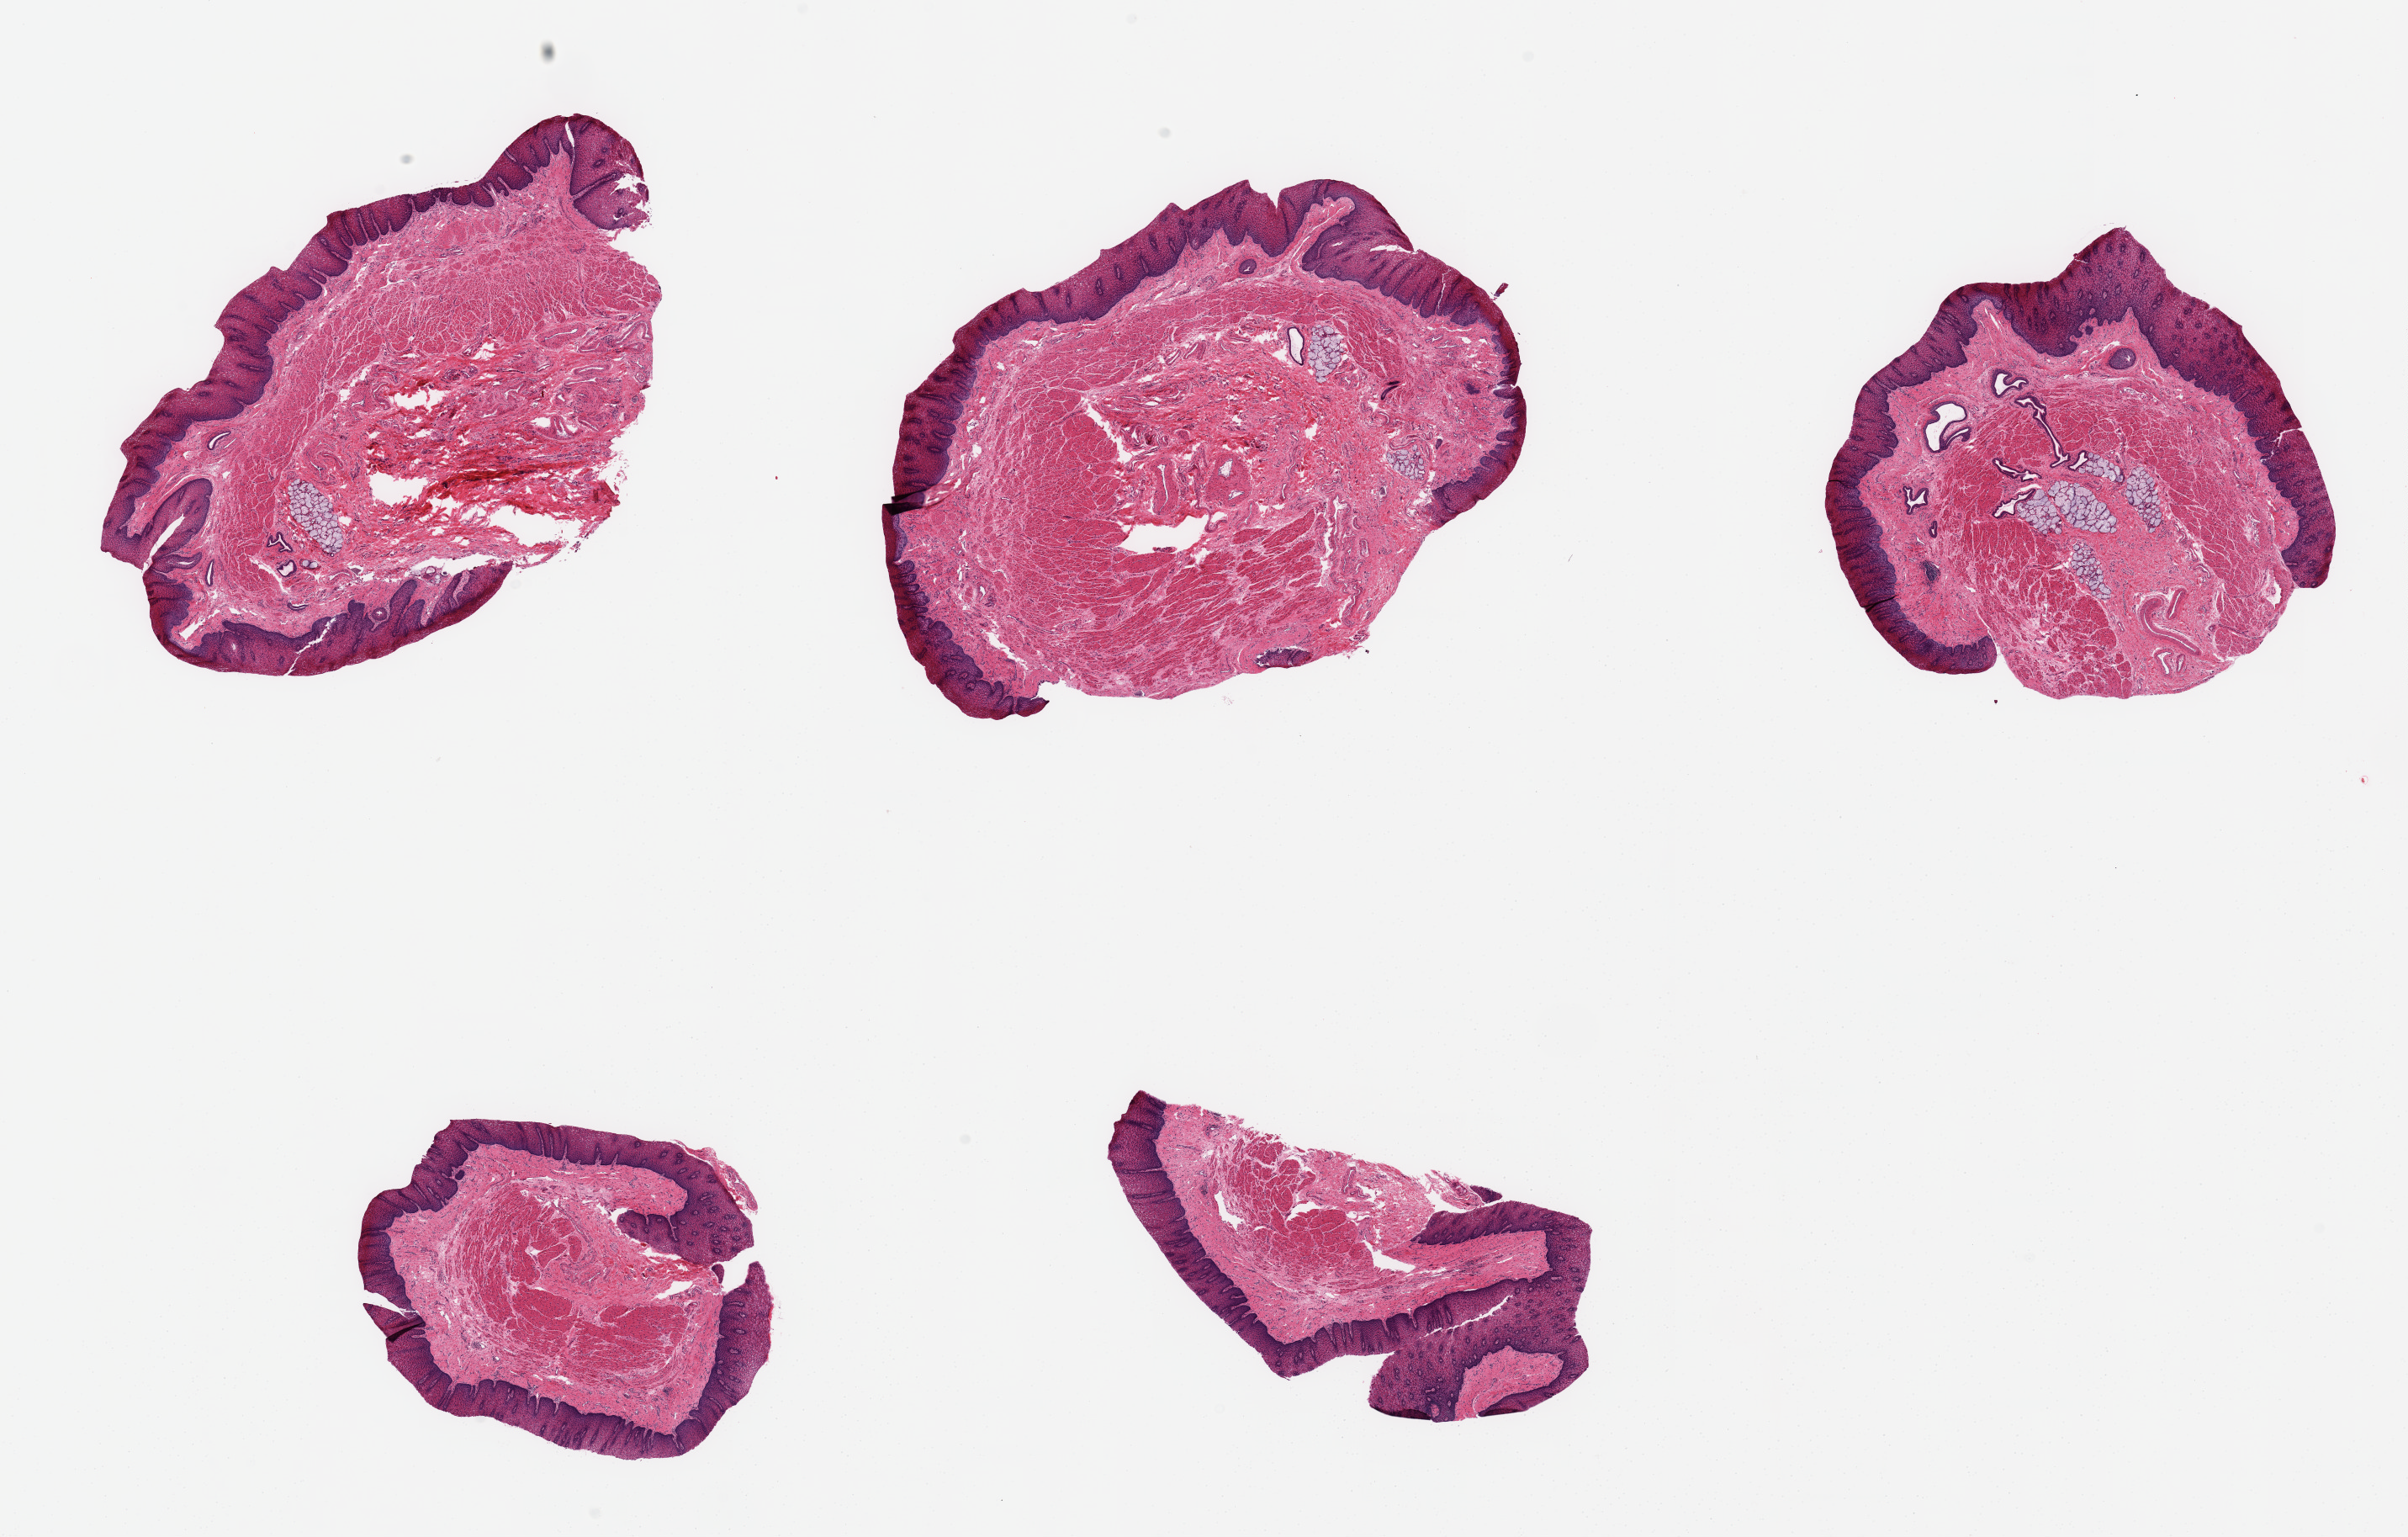
Digitized hematoxylin and eosin (H&E)-stained section, brightfield — low-resolution overview of the scanned area, about 22.6 x 14.4 mm (from a 20x scan), PAXgene-fixed, paraffin-embedded tissue, sampled site (target tissue): esophageal mucous membrane, tissue donor sample. Female donor.
Pathologist's review note for this sample: 5 pieces, squamous mucosa ~0.45mm, ~10% thickness; submucosal mucus glands present.